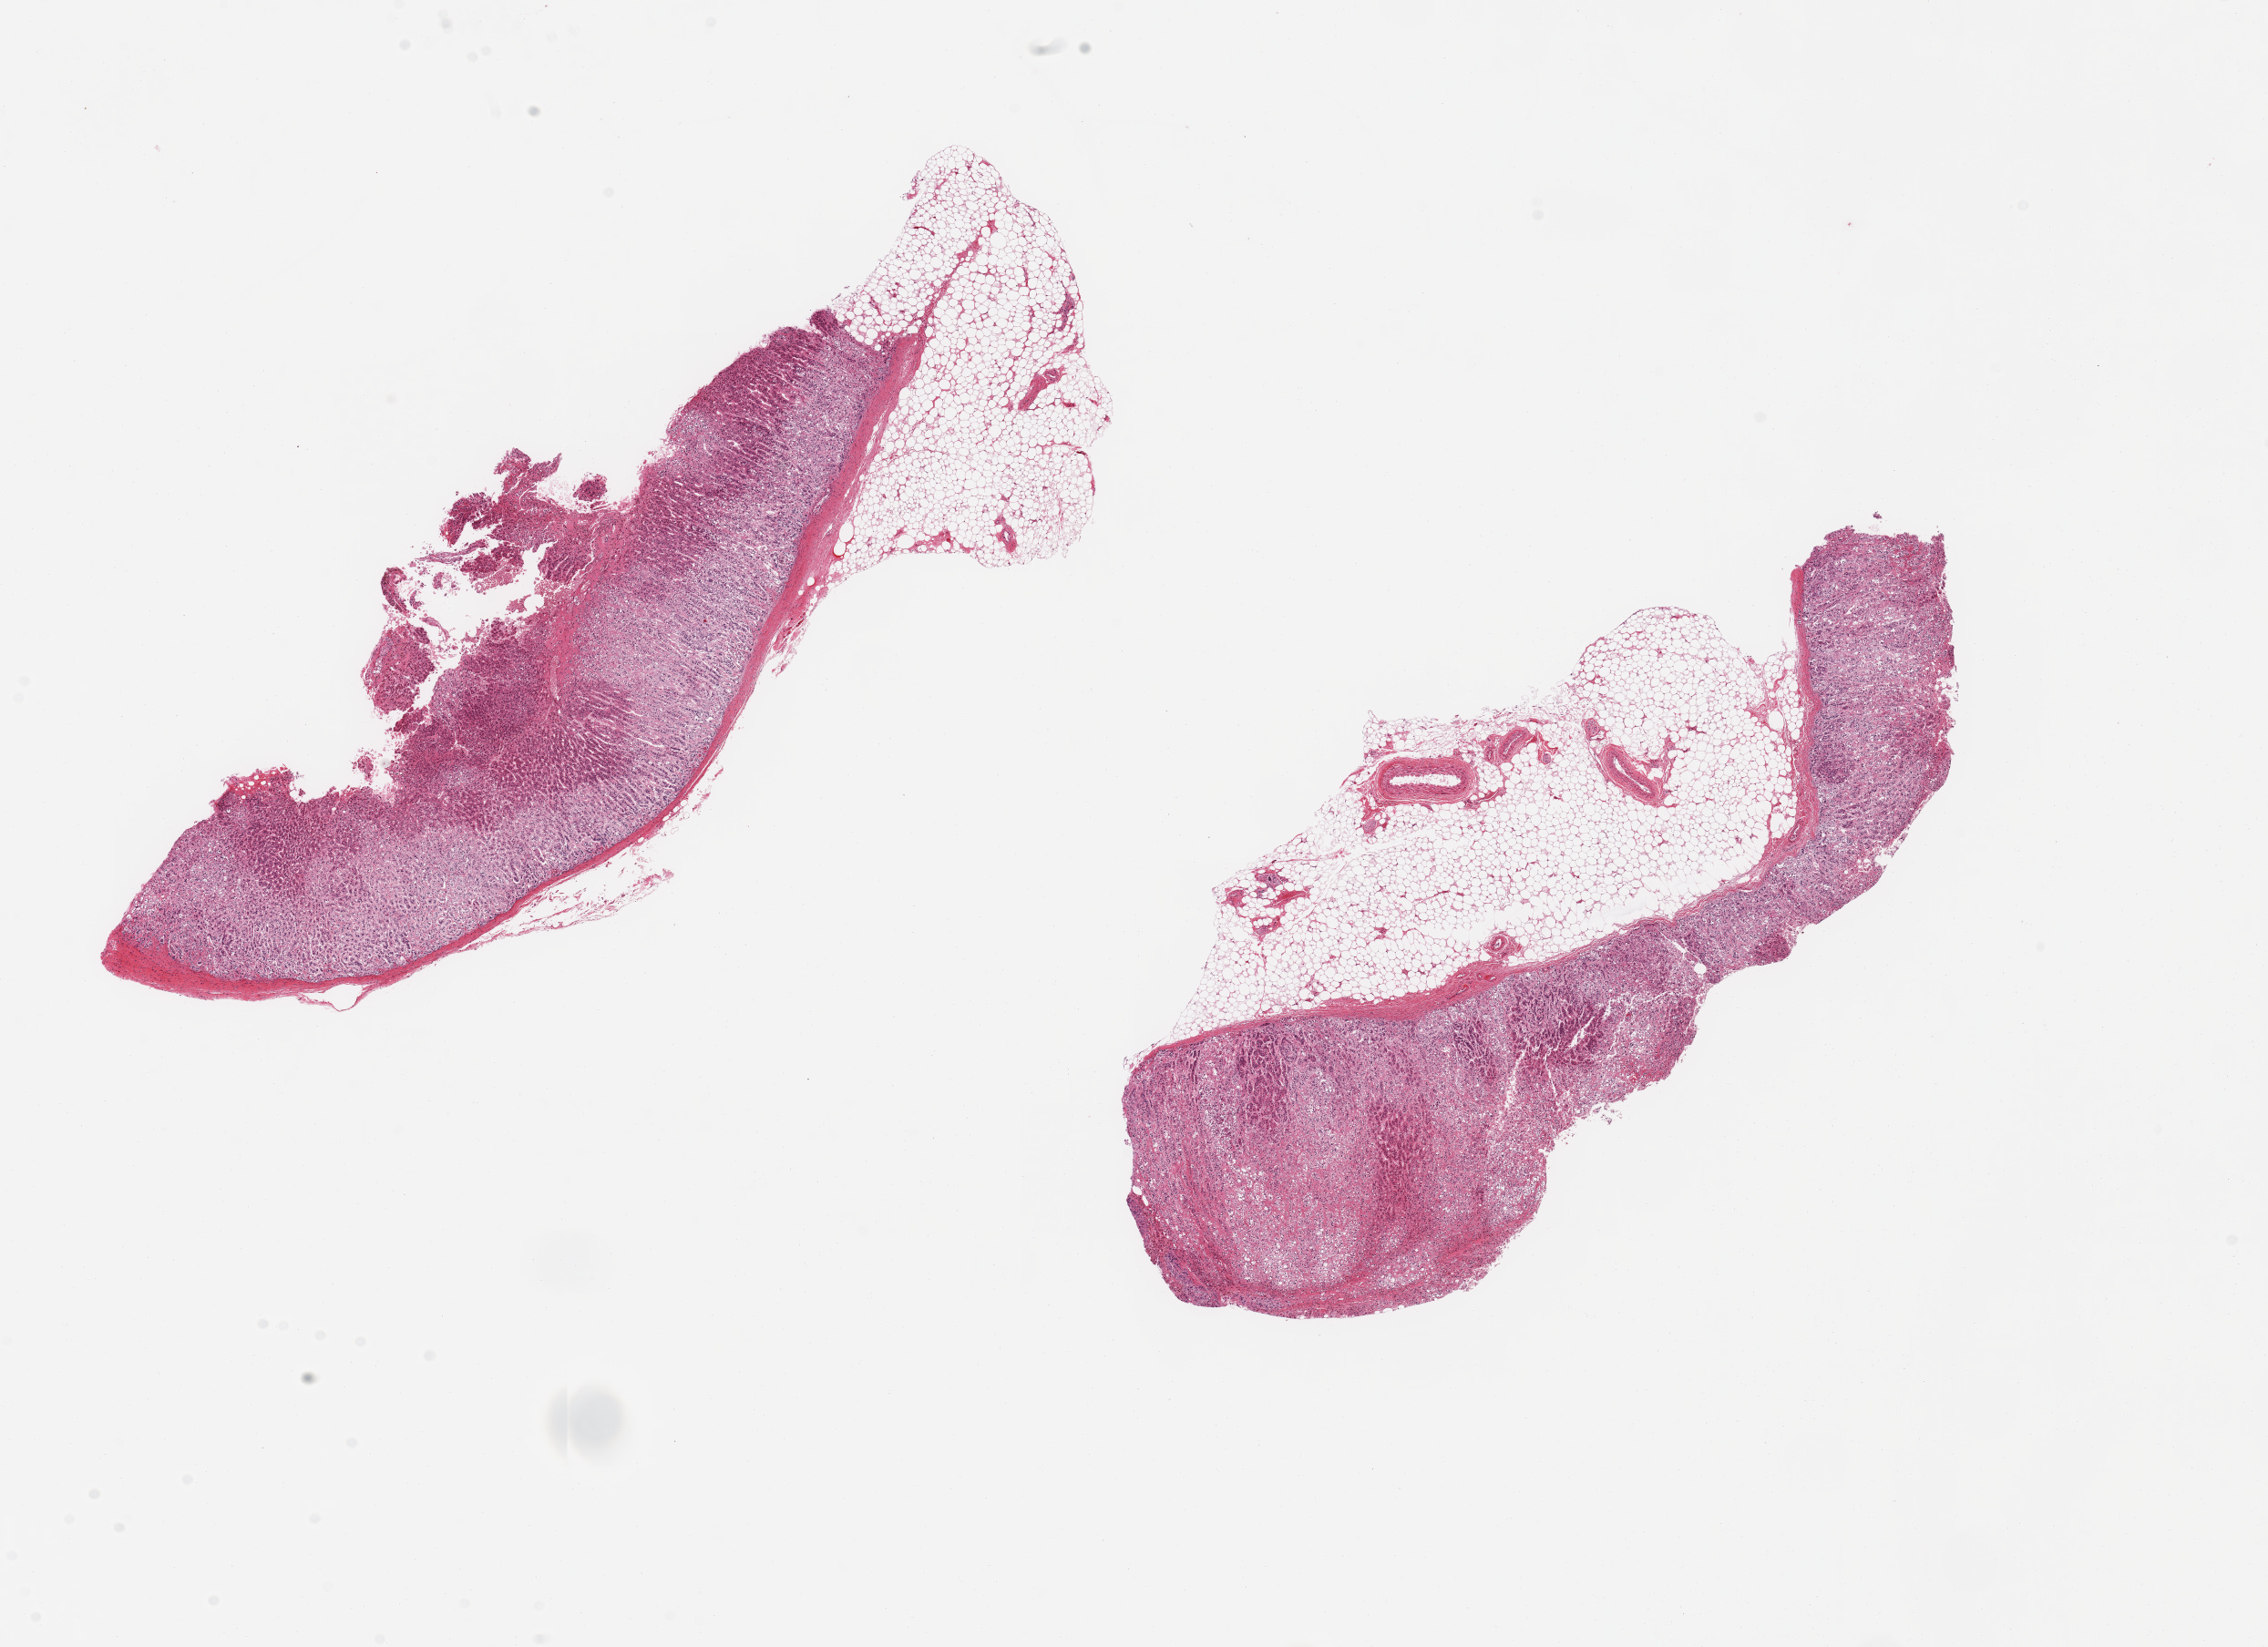
Whole-slide image, hematoxylin and eosin (H&E) stain, brightfield, a low-resolution overview of the entire scanned area, about 19.7 x 14.3 mm (acquisition: 20x scan), PAXgene-fixed paraffin-embedded (PFPE) section, target tissue: adrenal gland, donor tissue sample.
Review note (as recorded): 2 pieces,~9x2.6mm; 30-40% periadrenal fat.